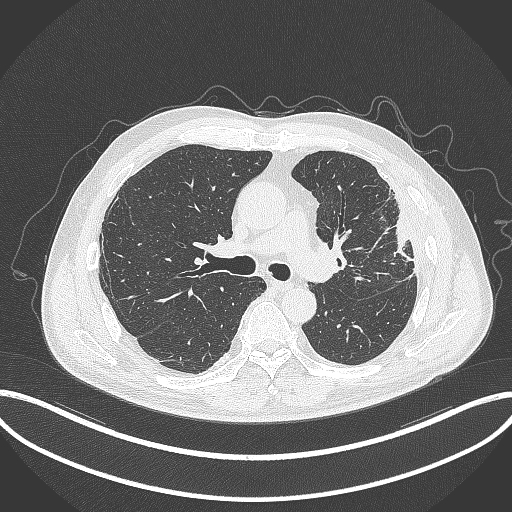
Chest CT, one axial slice. Slice 211 of 382 in the series (ordered by position). Reconstruction kernel B70f. Lung window (W 1500 / L -600 HU). 512 × 512 image matrix, field of view 415 × 415 mm. Male patient, age 64 years. Case-level facts recorded for this patient, not image findings: clinical TNM (as recorded): T4 N1 M0.
Annotated regions visible in this slice (rectangle marked by the reading radiologist):
- lung tumour (recorded histology: adenocarcinoma): box from (x=387, y=202) to (x=417, y=263) px